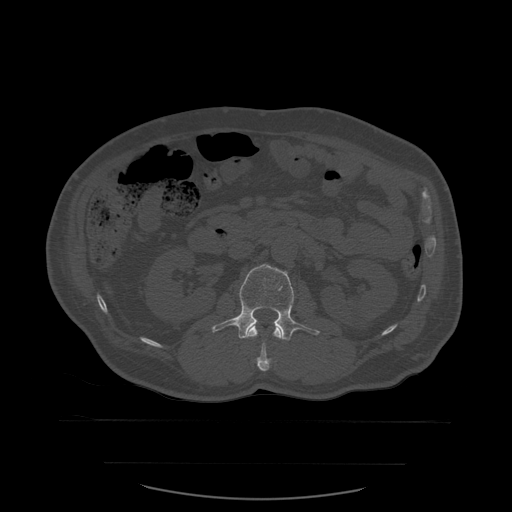
CT including the spine, one axial slice; position 227 of 590 along the scan axis; bone window (W 1800 / L 400 HU); 1.25 mm slice thickness; 512 × 512 image matrix, field of view 479 × 479 mm. Patient age 71 years. From the clinical record (not read from this slice): primary cancer: lung; vertebrae with lytic lesions (as recorded): T1, T2, L5, S1.
Annotated regions visible in this slice (semi-automatically segmented with operator editing):
- L1 vertebra: bounding box [x1, y1, x2, y2] px = [247, 326, 283, 372]
- L2 vertebra: [212, 264, 320, 341]